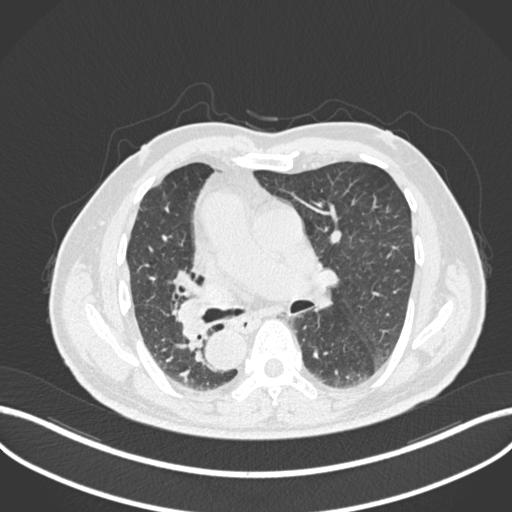
Chest CT, one axial slice. Position 122 of 206 along the scan axis. Reconstruction kernel B30f. 120 kVp. Lung window (W 1500 / L -600 HU). 1 mm slice thickness. 512 × 512 image matrix. Patient: male, 67 years. Case-level facts recorded for this patient, not image findings: clinical TNM (as recorded): T2a N0 M0.
Structures marked on this image (rectangle marked by the reading radiologist):
- lung tumour (recorded histology: squamous cell carcinoma): box from (x=173, y=293) to (x=210, y=343) px